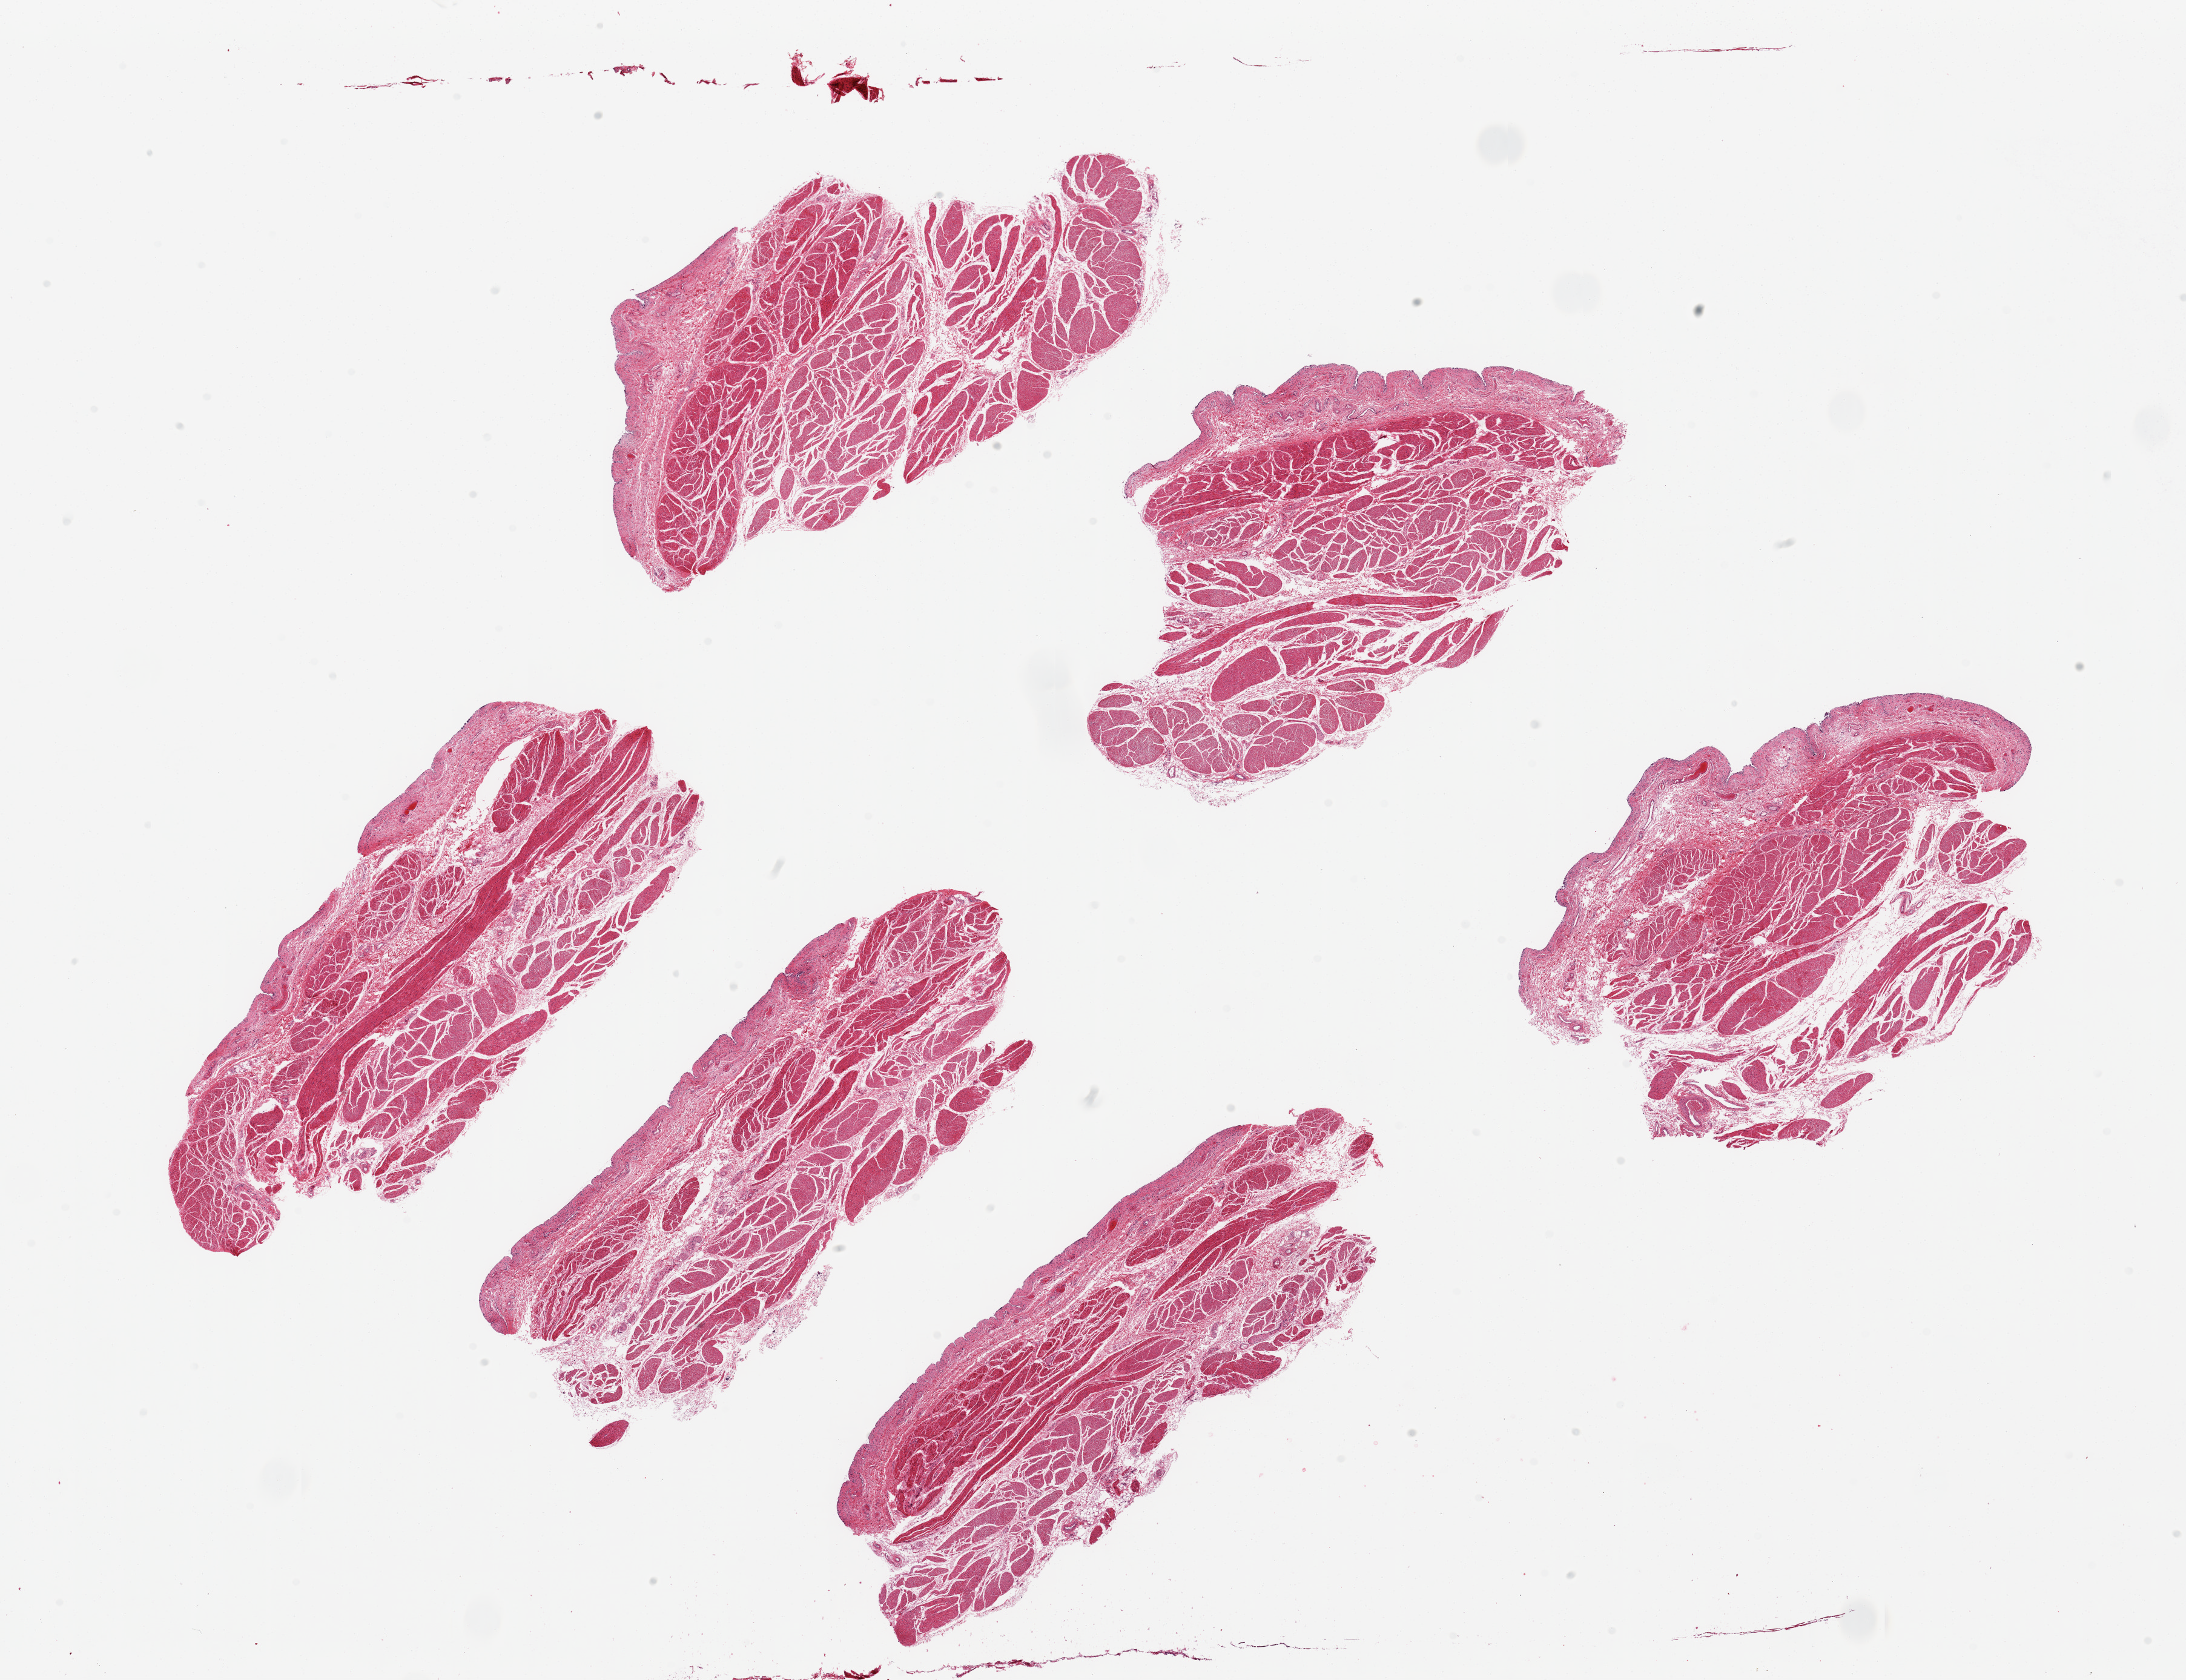
Digitized hematoxylin and eosin (H&E)-stained section — a low-resolution overview of the entire scanned area, about 28.5 x 21.9 mm (acquisition: 20x scan), PAXgene-fixed paraffin-embedded (PFPE) section, sampled site (target tissue): urinary bladder, tissue donor sample. Male donor.
Pathologist's review note for this sample: 6 pieces up to 8.6x5; mucosa on all, but sloughed (3); muscle preserved (1).